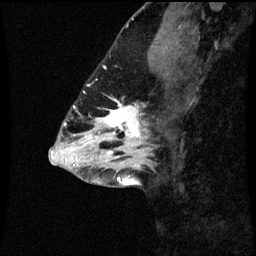
Breast MRI (dynamic contrast-enhanced), one sagittal slice; dynamic contrast-enhanced series, image 2 of 3 at this slice position (ordered by acquisition); 1.5 T; TE 4.2 ms, TR 8.9 ms; 2 mm slice thickness; 256 × 256 image matrix, field of view 200 × 200 mm. Female patient, age 43 years. From the clinical record (not read from this slice): setting: breast cancer imaged before/during neoadjuvant chemotherapy; receptor status: HR-positive, HER2-negative.
Structures marked on this image (semi-automatically segmented with operator editing):
- analysis volume of interest (the breast-tissue region the enhancement analysis was run in; not a lesion): bounding box <96,98,159,159> (left, top, right, bottom; pixels)
- tumour enhancement mask (voxels above the 70 % enhancement threshold inside the analysis volume of interest): <104,102,149,155>